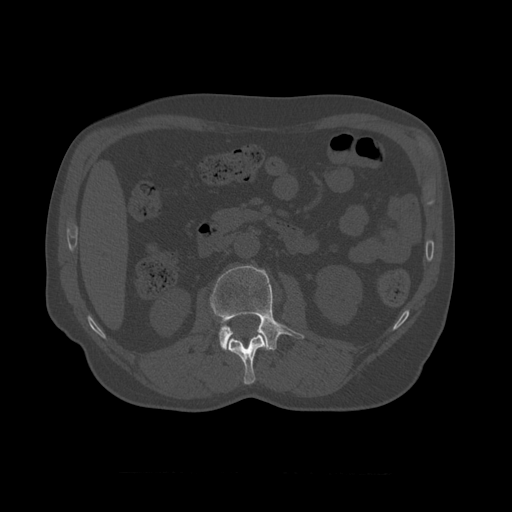
CT including the spine, one axial slice. Slice 340 of 450 in the series (ordered by position). Bone window (W 1800 / L 400 HU). 1.25 mm slice thickness. 512 × 512 image matrix. Patient age 75 years. Case-level facts recorded for this patient, not image findings: primary cancer: prostate.
Structures marked on this image (semi-automatically segmented with operator editing):
- L1 vertebra: bounding box <228,334,269,385> (left, top, right, bottom; pixels)
- L2 vertebra: <210,265,305,351>